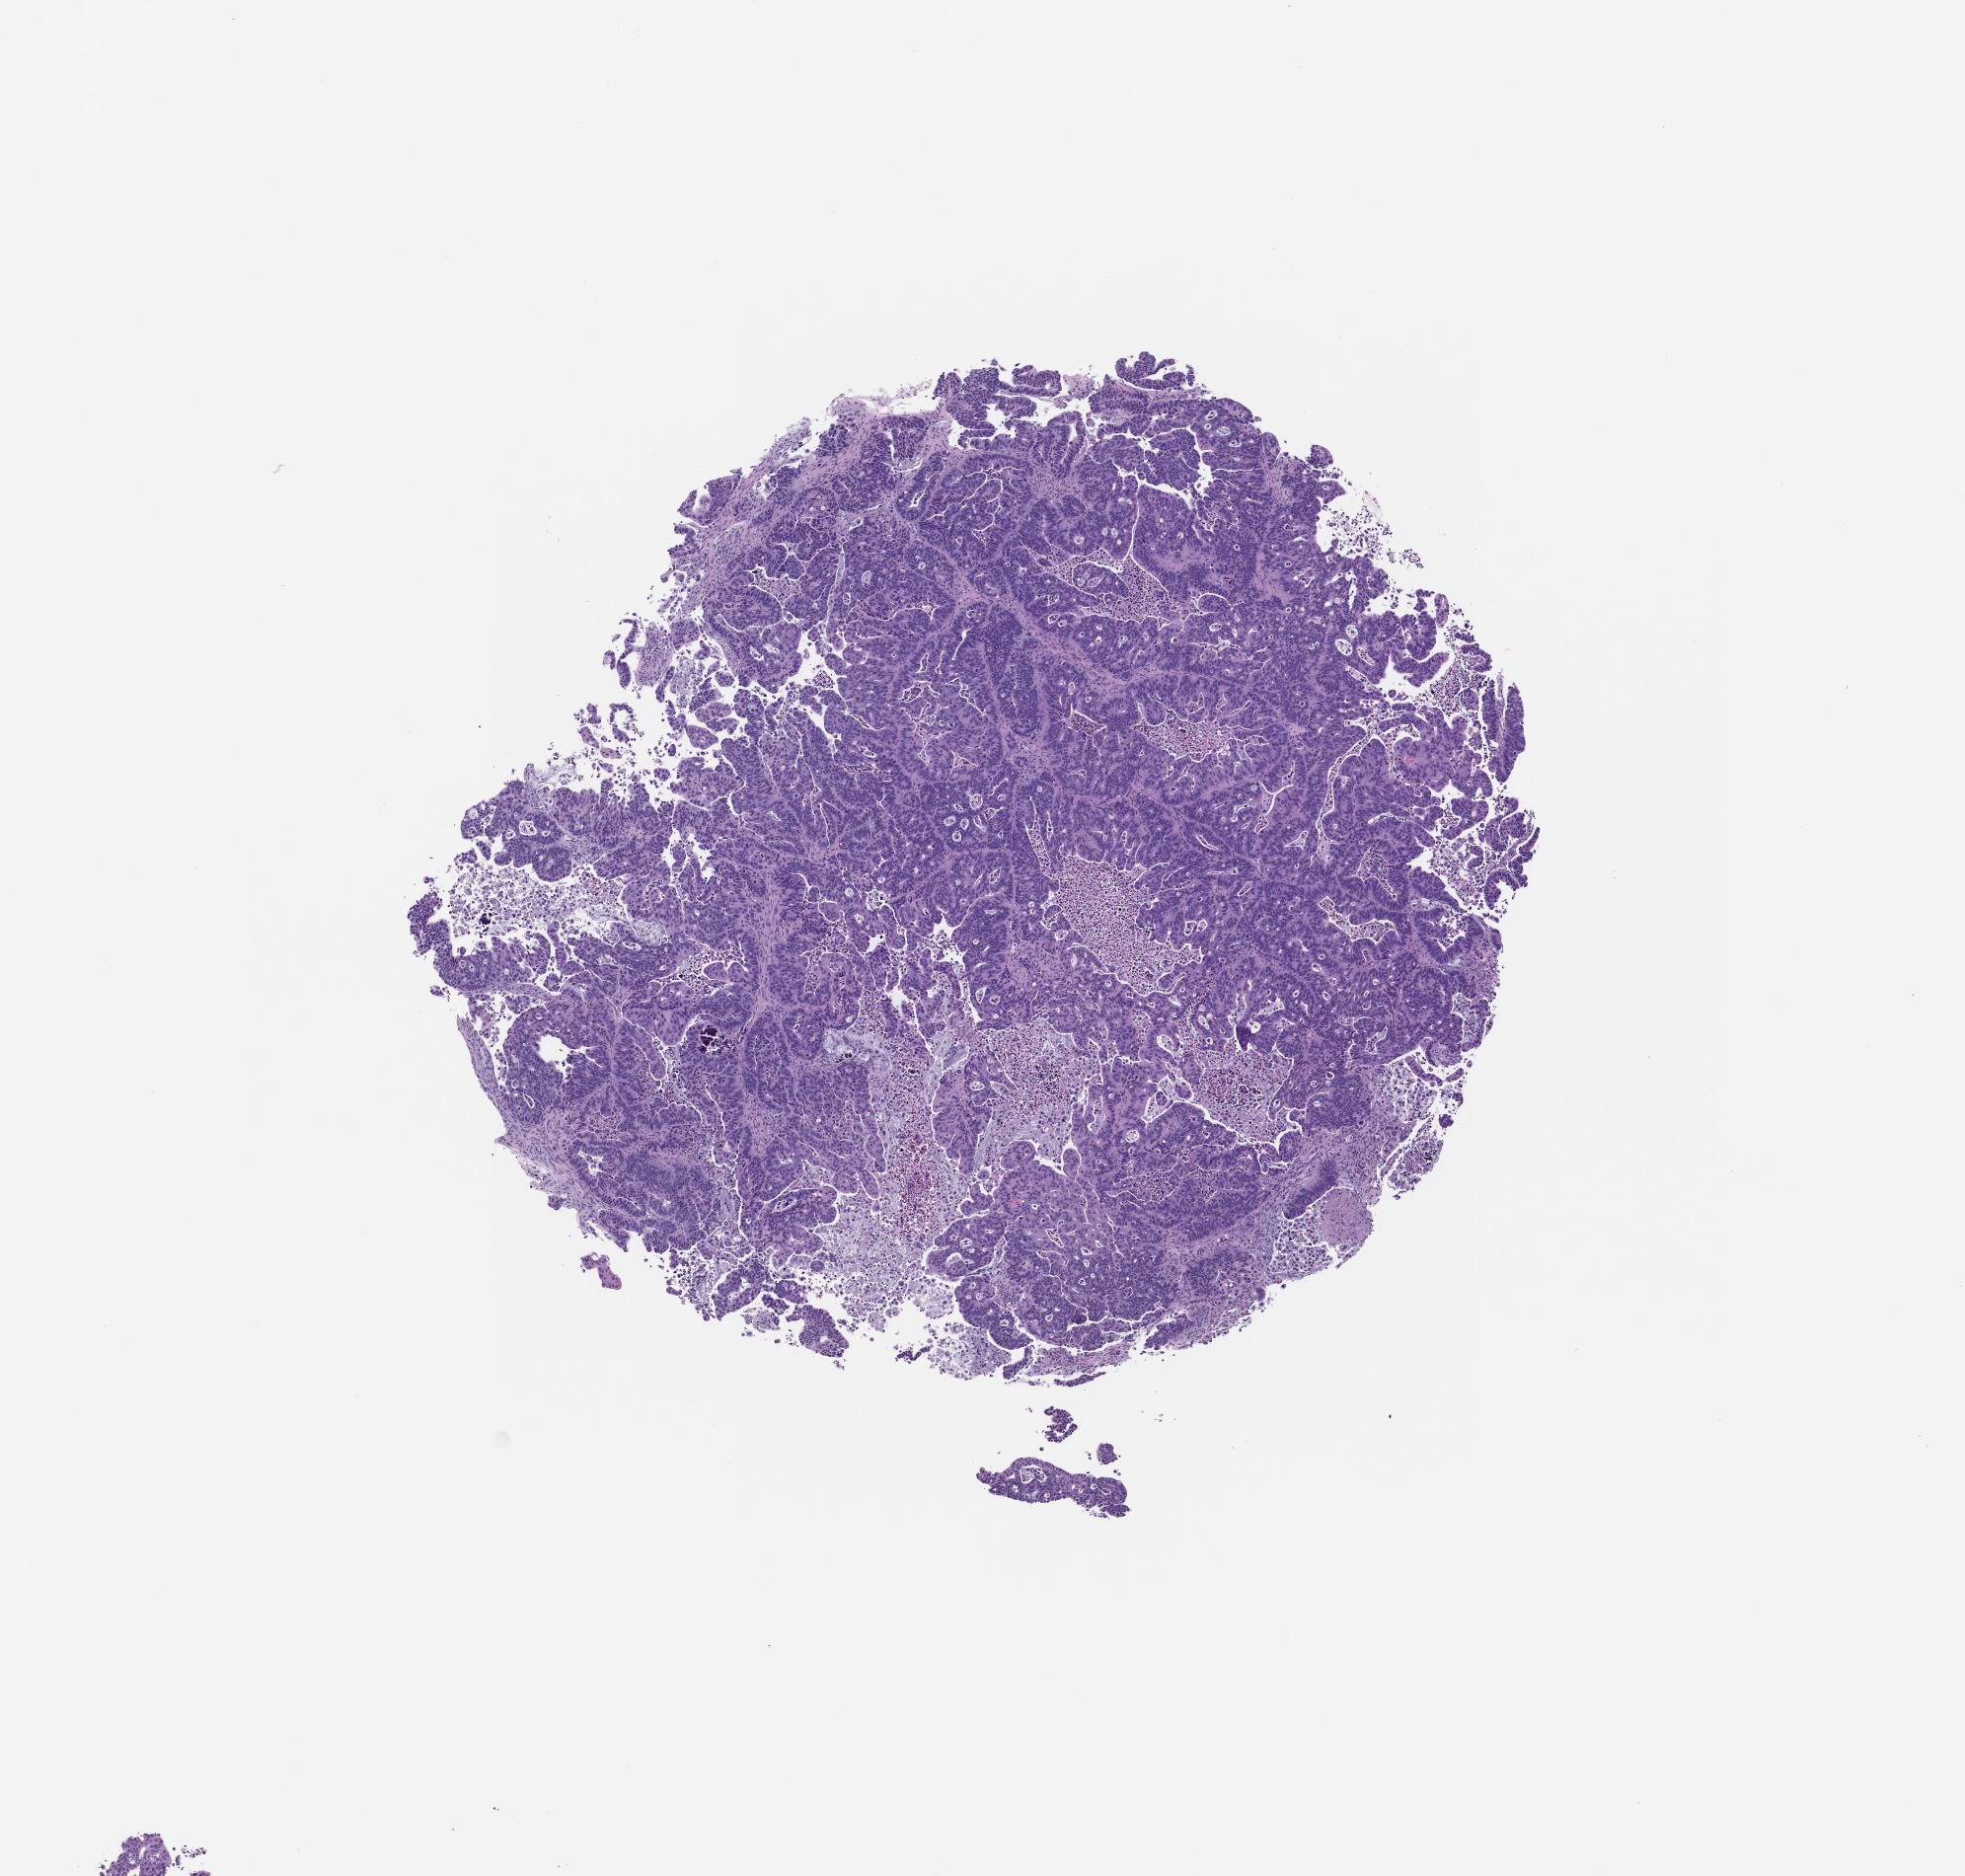
Whole-slide image, hematoxylin and eosin (H&E): patient-derived xenograft (human tumor grown in a mouse), passage 0, a low-resolution overview of the entire scanned area, about 8.0 x 7.6 mm. FFPE section. Originating tumor site category: colon.
Originating patient diagnosis: Colon Adenocarcinoma.